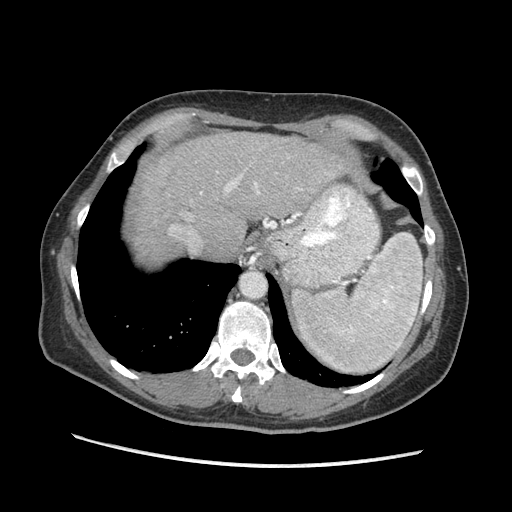
Contrast-enhanced abdominal CT (liver protocol), one axial slice. Position 149 of 170 along the scan axis. Soft-tissue window (W 400 / L 40 HU). 2.5 mm slice thickness. 512 × 512 image matrix, field of view 360 × 360 mm. From the clinical record (not read from this slice): diagnosis: hepatocellular carcinoma (patient treated with transarterial chemoembolisation; whether this scan precedes or follows treatment is not stated here); TNM stage (as recorded): Stage-II; Child-Pugh class: A; tumour differentiation: no biopsy; tumour nodularity: multinodular.
Outlined on this slice (semi-automatically segmented with operator editing):
- abdominal aorta: bounding box <241,272,264,297> (left, top, right, bottom; pixels)
- liver parenchyma outside the tumour (the mass and vessels are separate outlines, so this box may not span the whole liver): <128,132,358,264>
- liver vessels: <170,175,302,230>